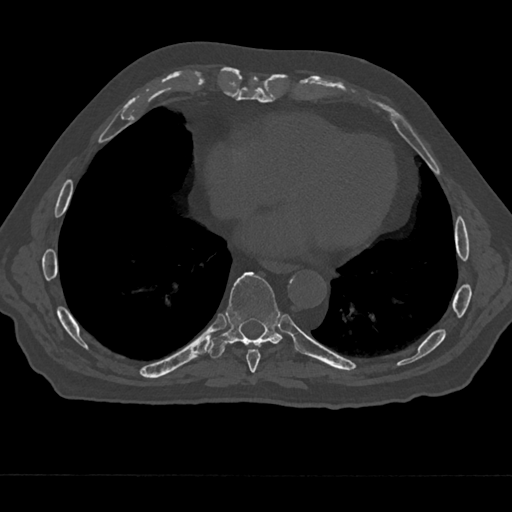
CT including the spine, one axial slice; slice 281 of 797 in the series (ordered by position); reconstruction kernel Br40s/3; bone window (W 1800 / L 400 HU); 0.5 mm slice thickness; 512 × 512 image matrix, field of view 377 × 377 mm. Patient: male, 75 years. From the clinical record (not read from this slice): primary cancer: renal; vertebrae with lytic lesions (as recorded): T4.
Outlined on this slice (semi-automatic segmentation, software-assisted and operator-edited):
- T8 vertebra: bounding box <246,349,261,373> (left, top, right, bottom; pixels)
- T9 vertebra: <207,272,296,358>